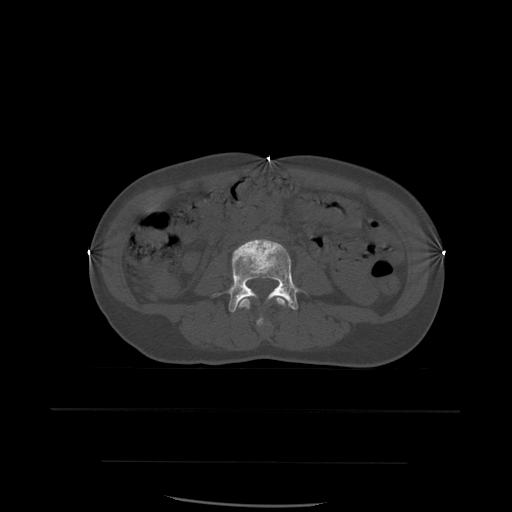
CT including the spine, one axial slice. Bone window (W 1800 / L 400 HU). 512 × 512 image matrix. Patient age 48 years. From the clinical record (not read from this slice): primary cancer: lung; vertebrae with lytic lesions (as recorded): T11.
Outlined on this slice (semi-automatically segmented with operator editing):
- L3 vertebra: bounding box <236,297,289,327> (left, top, right, bottom; pixels)
- L4 vertebra: <214,239,300,313>